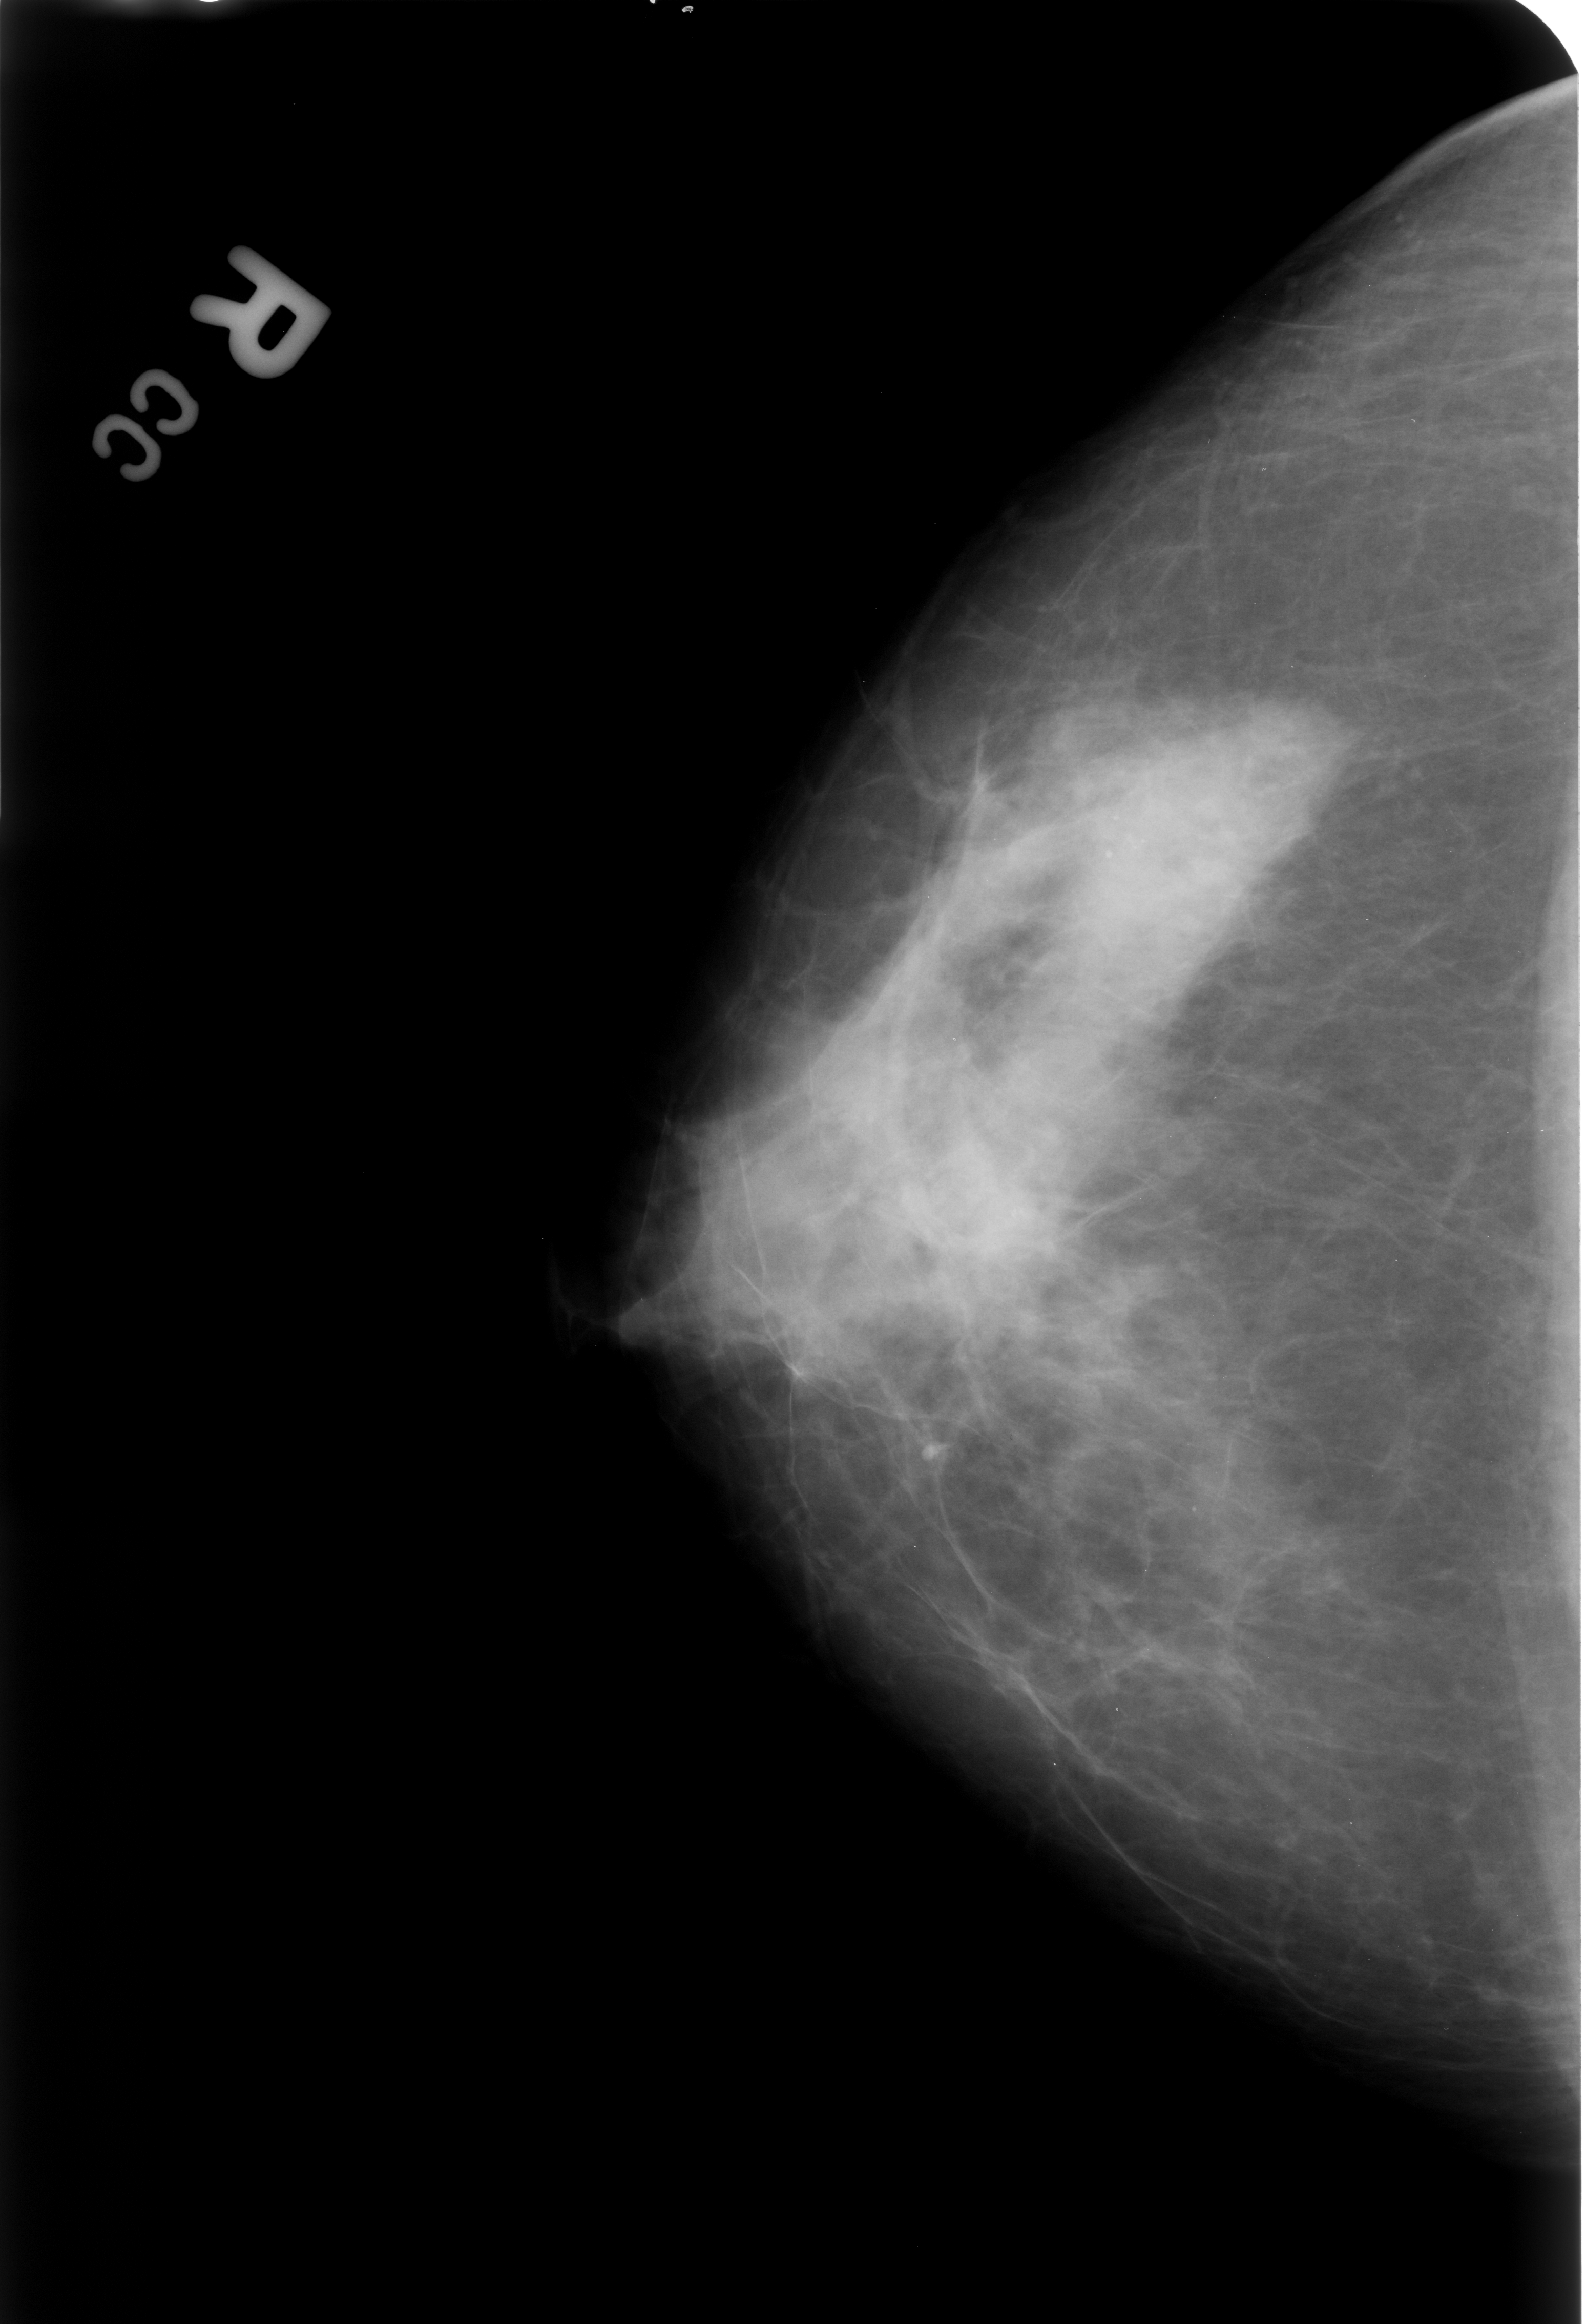
Scanned film-screen mammogram. Right breast. CC view. 1586 × 2324 image matrix.
Marked abnormalities (boxes around the expert regions of interest):
- Finding 1 of 2: calcifications, morphology punctate / round and regular, distribution regional; BI-RADS assessment category 2; outcome (as recorded, no biopsy): benign without callback (not worked up further): bounding box (x1, y1, x2, y2) in pixels: (979, 905, 1042, 1005)
- Finding 2 of 2: calcifications, morphology punctate / round and regular, distribution regional; BI-RADS assessment category 2; subtlety rating 3 on a 1 (subtle) to 5 (obvious) scale; outcome (as recorded, no biopsy): benign without callback (not worked up further): (1049, 606, 1132, 706)